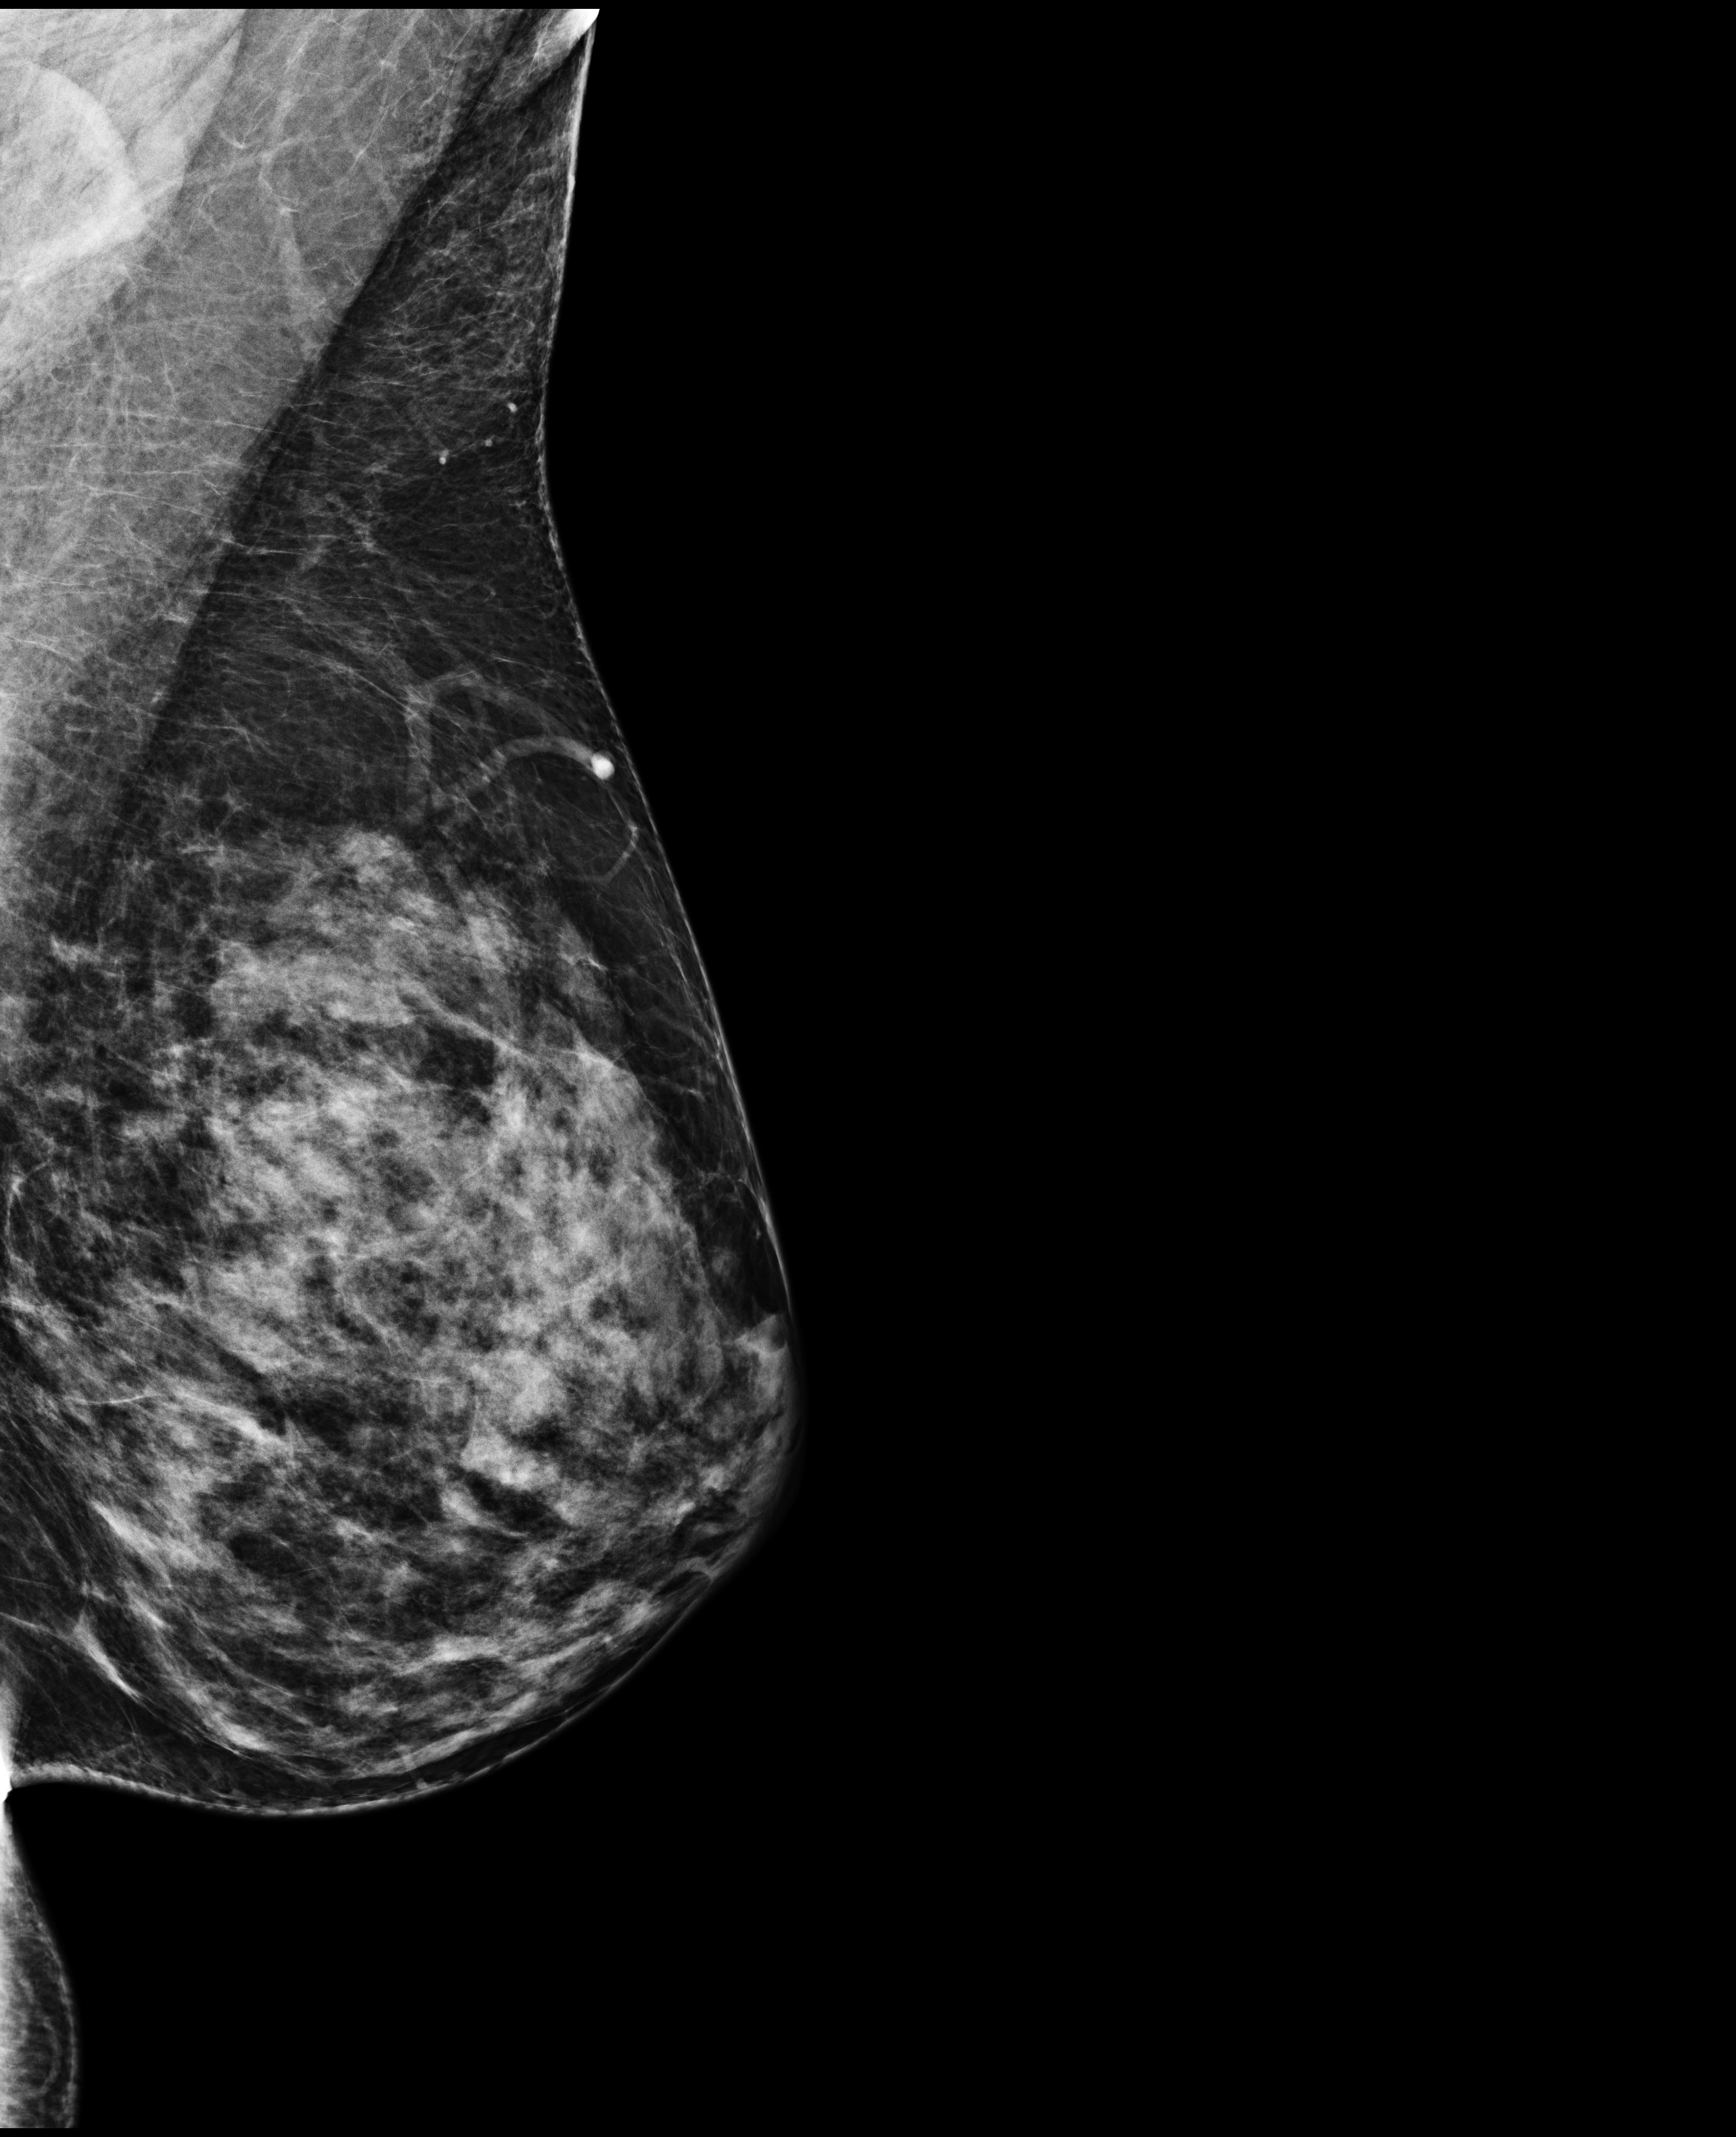
Screening examination. Female patient, age 43 years.
Image type: full-field digital mammogram. Breast: left. Projection: mediolateral oblique (MLO) view.